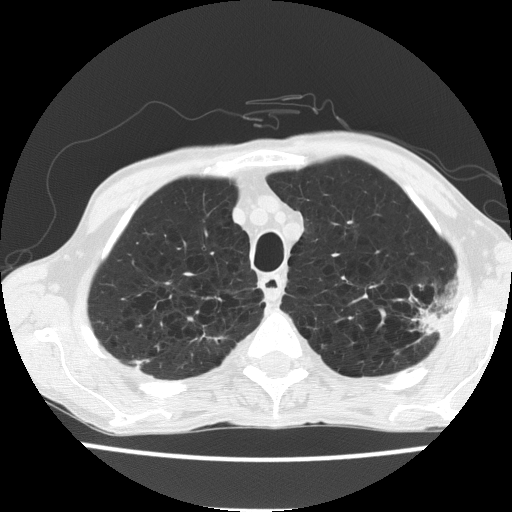
Chest CT (low-dose screening protocol), one axial image, baseline screening round, lung window (W 1500 / L -600 HU), 2 mm slice thickness, slice 36 of 187 in the series. Male participant, aged 60 years at enrolment. Current smoker at enrolment.
Lesion marked by an expert reader, bounding box (x1, y1, x2, y2) in pixels: (395, 281, 460, 347). Screening reader's record for this exam: no non-calcified nodule ≥4 mm recorded. Participant outcome: lung cancer diagnosed 490 days after this screen (after the second annual screen) — bronchiolo-alveolar carcinoma, mucinous, left upper lobe, stage IV (AJCC 6th edition).